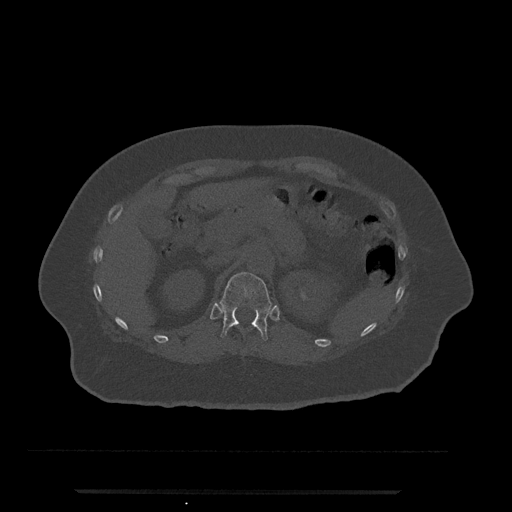
CT including the spine, one axial slice; position 180 of 797 along the scan axis; bone window (W 1800 / L 400 HU); 512 × 512 image matrix, field of view 440 × 440 mm. Female patient, age 51 years. From the clinical record (not read from this slice): primary cancer: neuro.
Structures marked on this image (semi-automatic segmentation, software-assisted and operator-edited):
- T12 vertebra: bounding box [x1, y1, x2, y2] px = [220, 272, 272, 341]